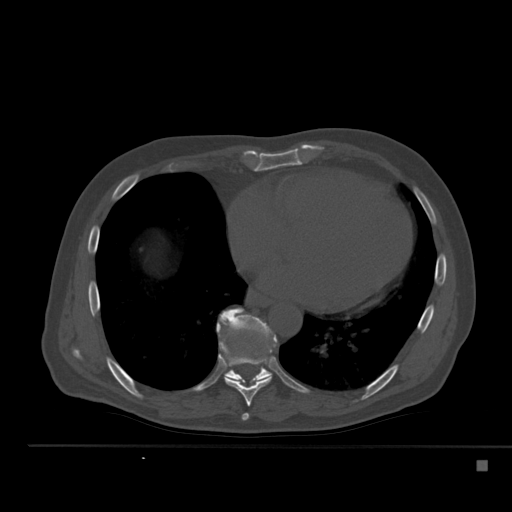
CT including the spine, one axial slice; slice 301 of 517 in the series (ordered by position); bone window (W 1800 / L 400 HU); 512 × 512 image matrix. Male patient, age 70 years. From the clinical record (not read from this slice): primary cancer: renal; vertebrae with lytic lesions (as recorded): T4, T6, T10, T12, L3, L4, L5.
Structures marked on this image (semi-automatic segmentation, software-assisted and operator-edited):
- T7 vertebra: bounding box [x1, y1, x2, y2] px = [242, 413, 249, 421]
- T8 vertebra: [216, 318, 277, 407]
- T9 vertebra: [219, 309, 277, 383]